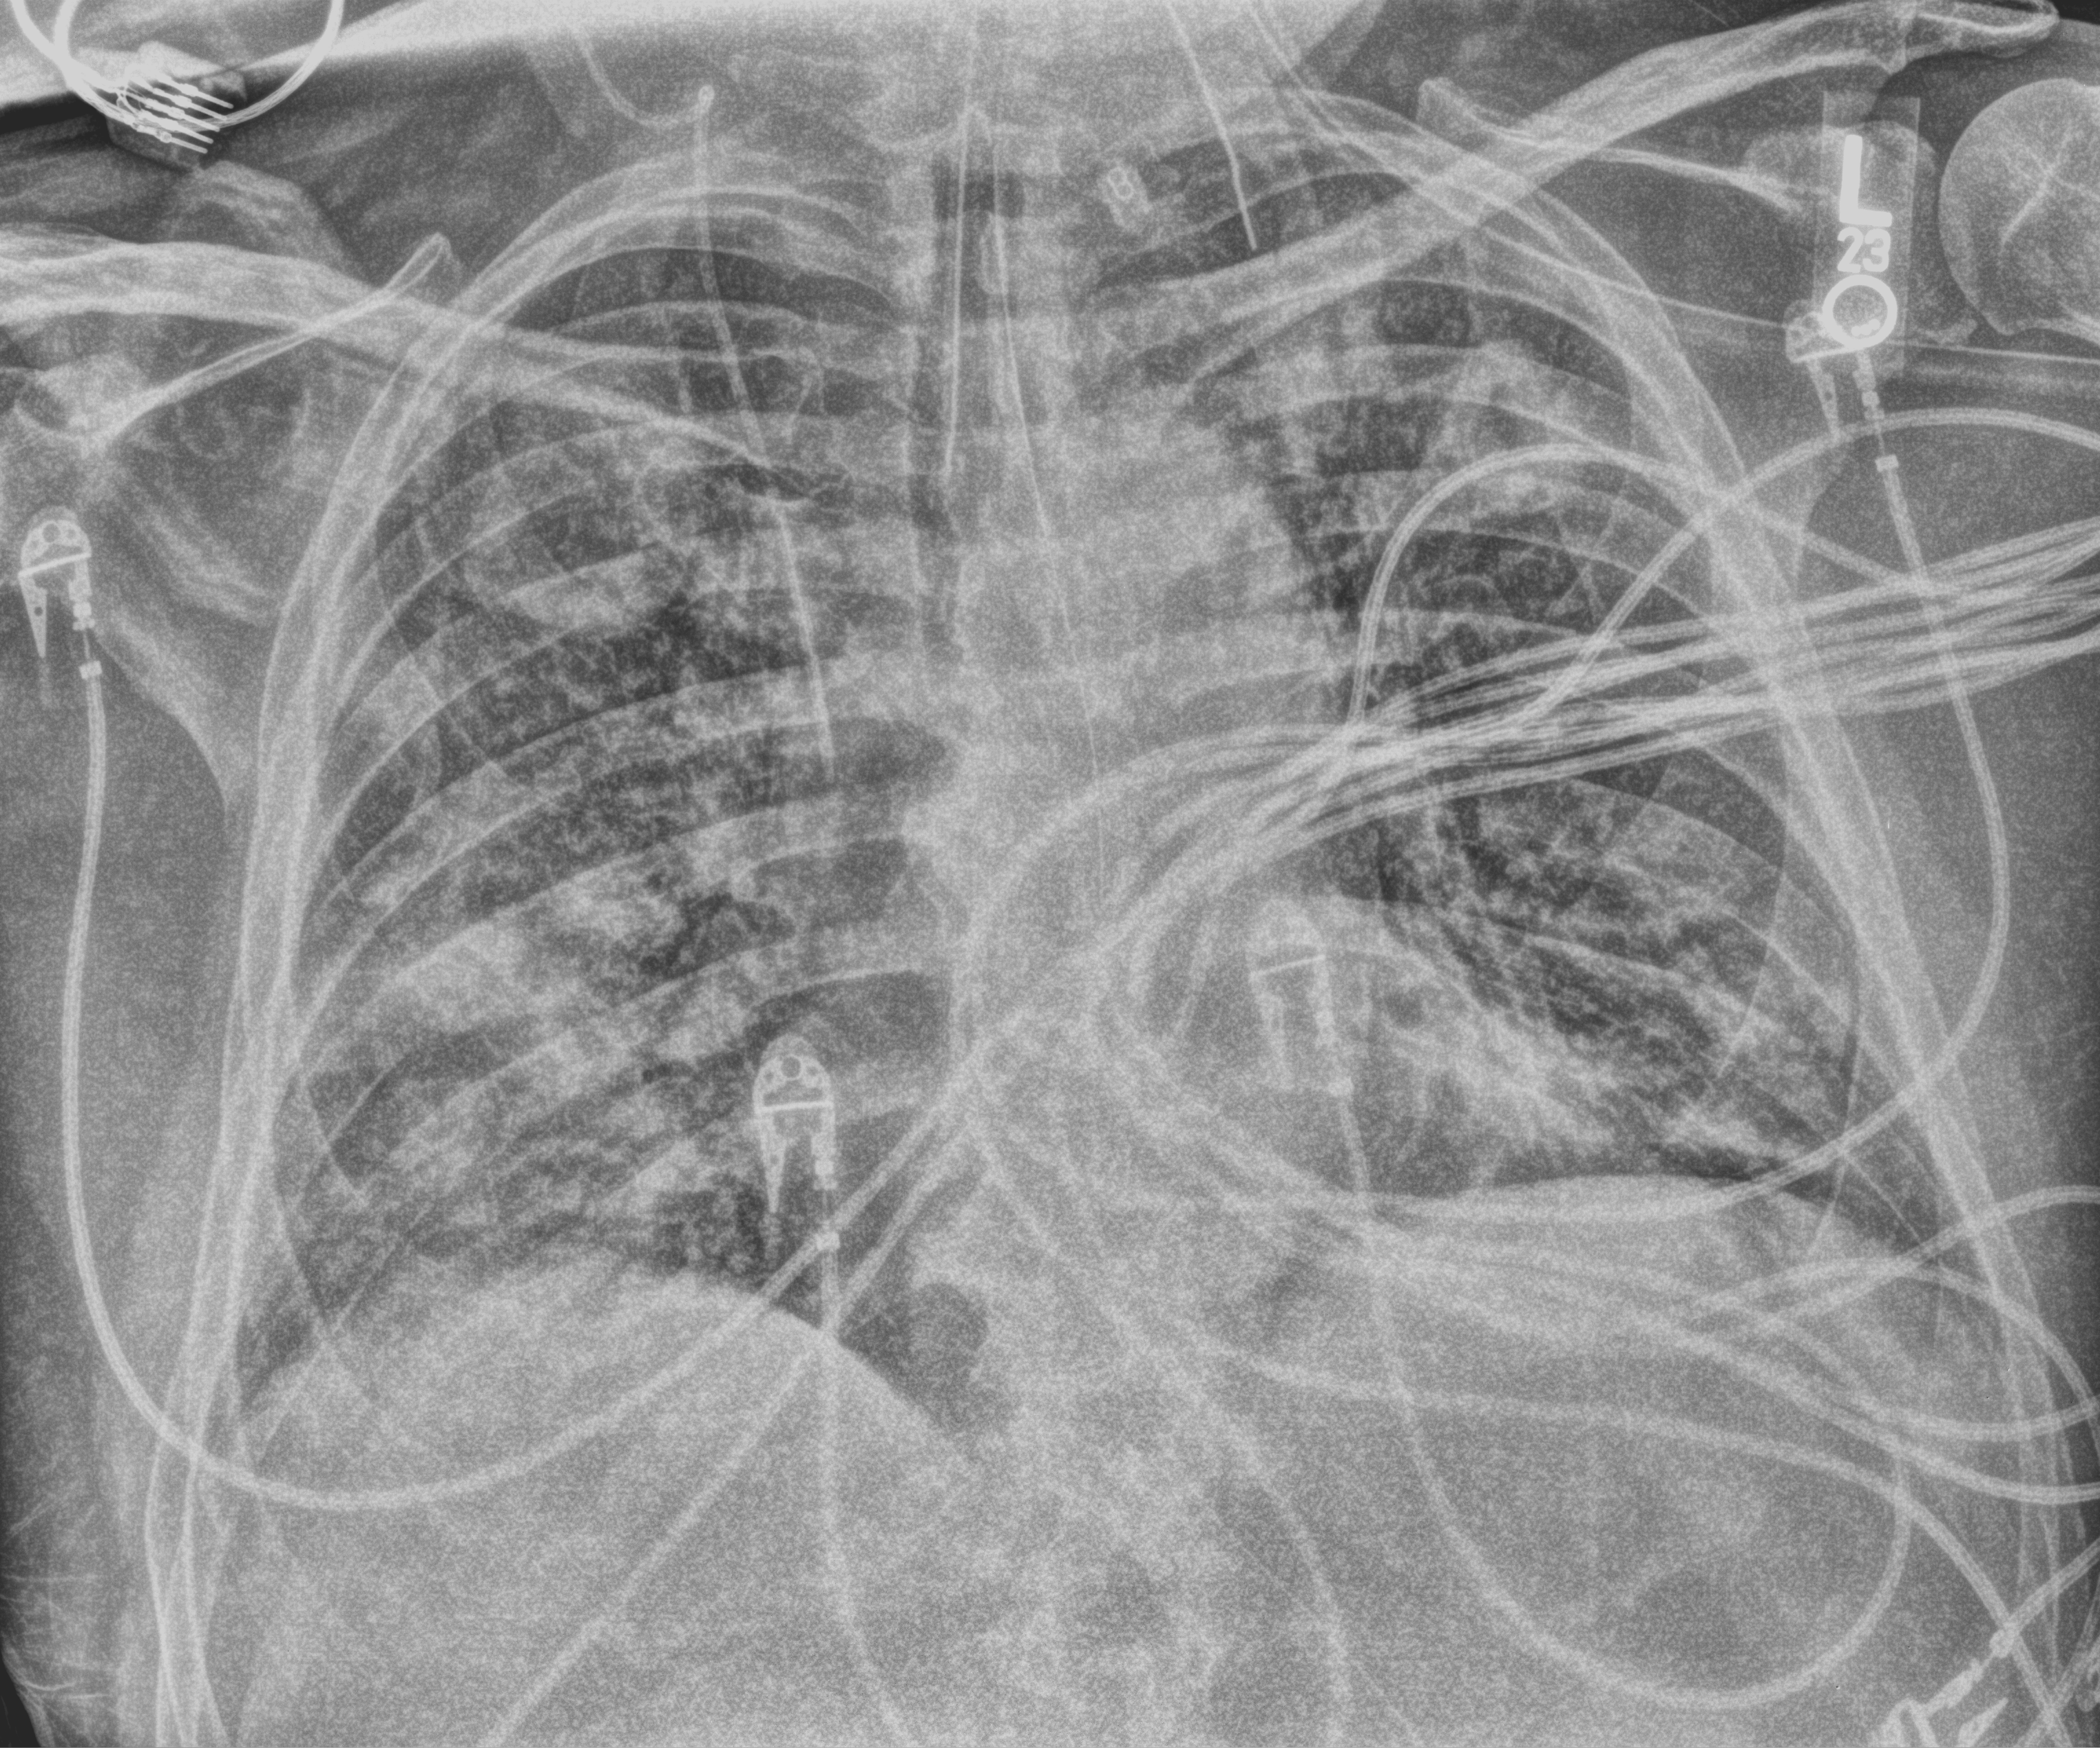
Portable chest radiograph. Patient hospitalised with COVID-19; male, aged 60–74 years.
From the hospital-stay record, not from the radiograph (when in the stay this image was taken is not recorded): admitted to intensive care during this hospital stay: yes.